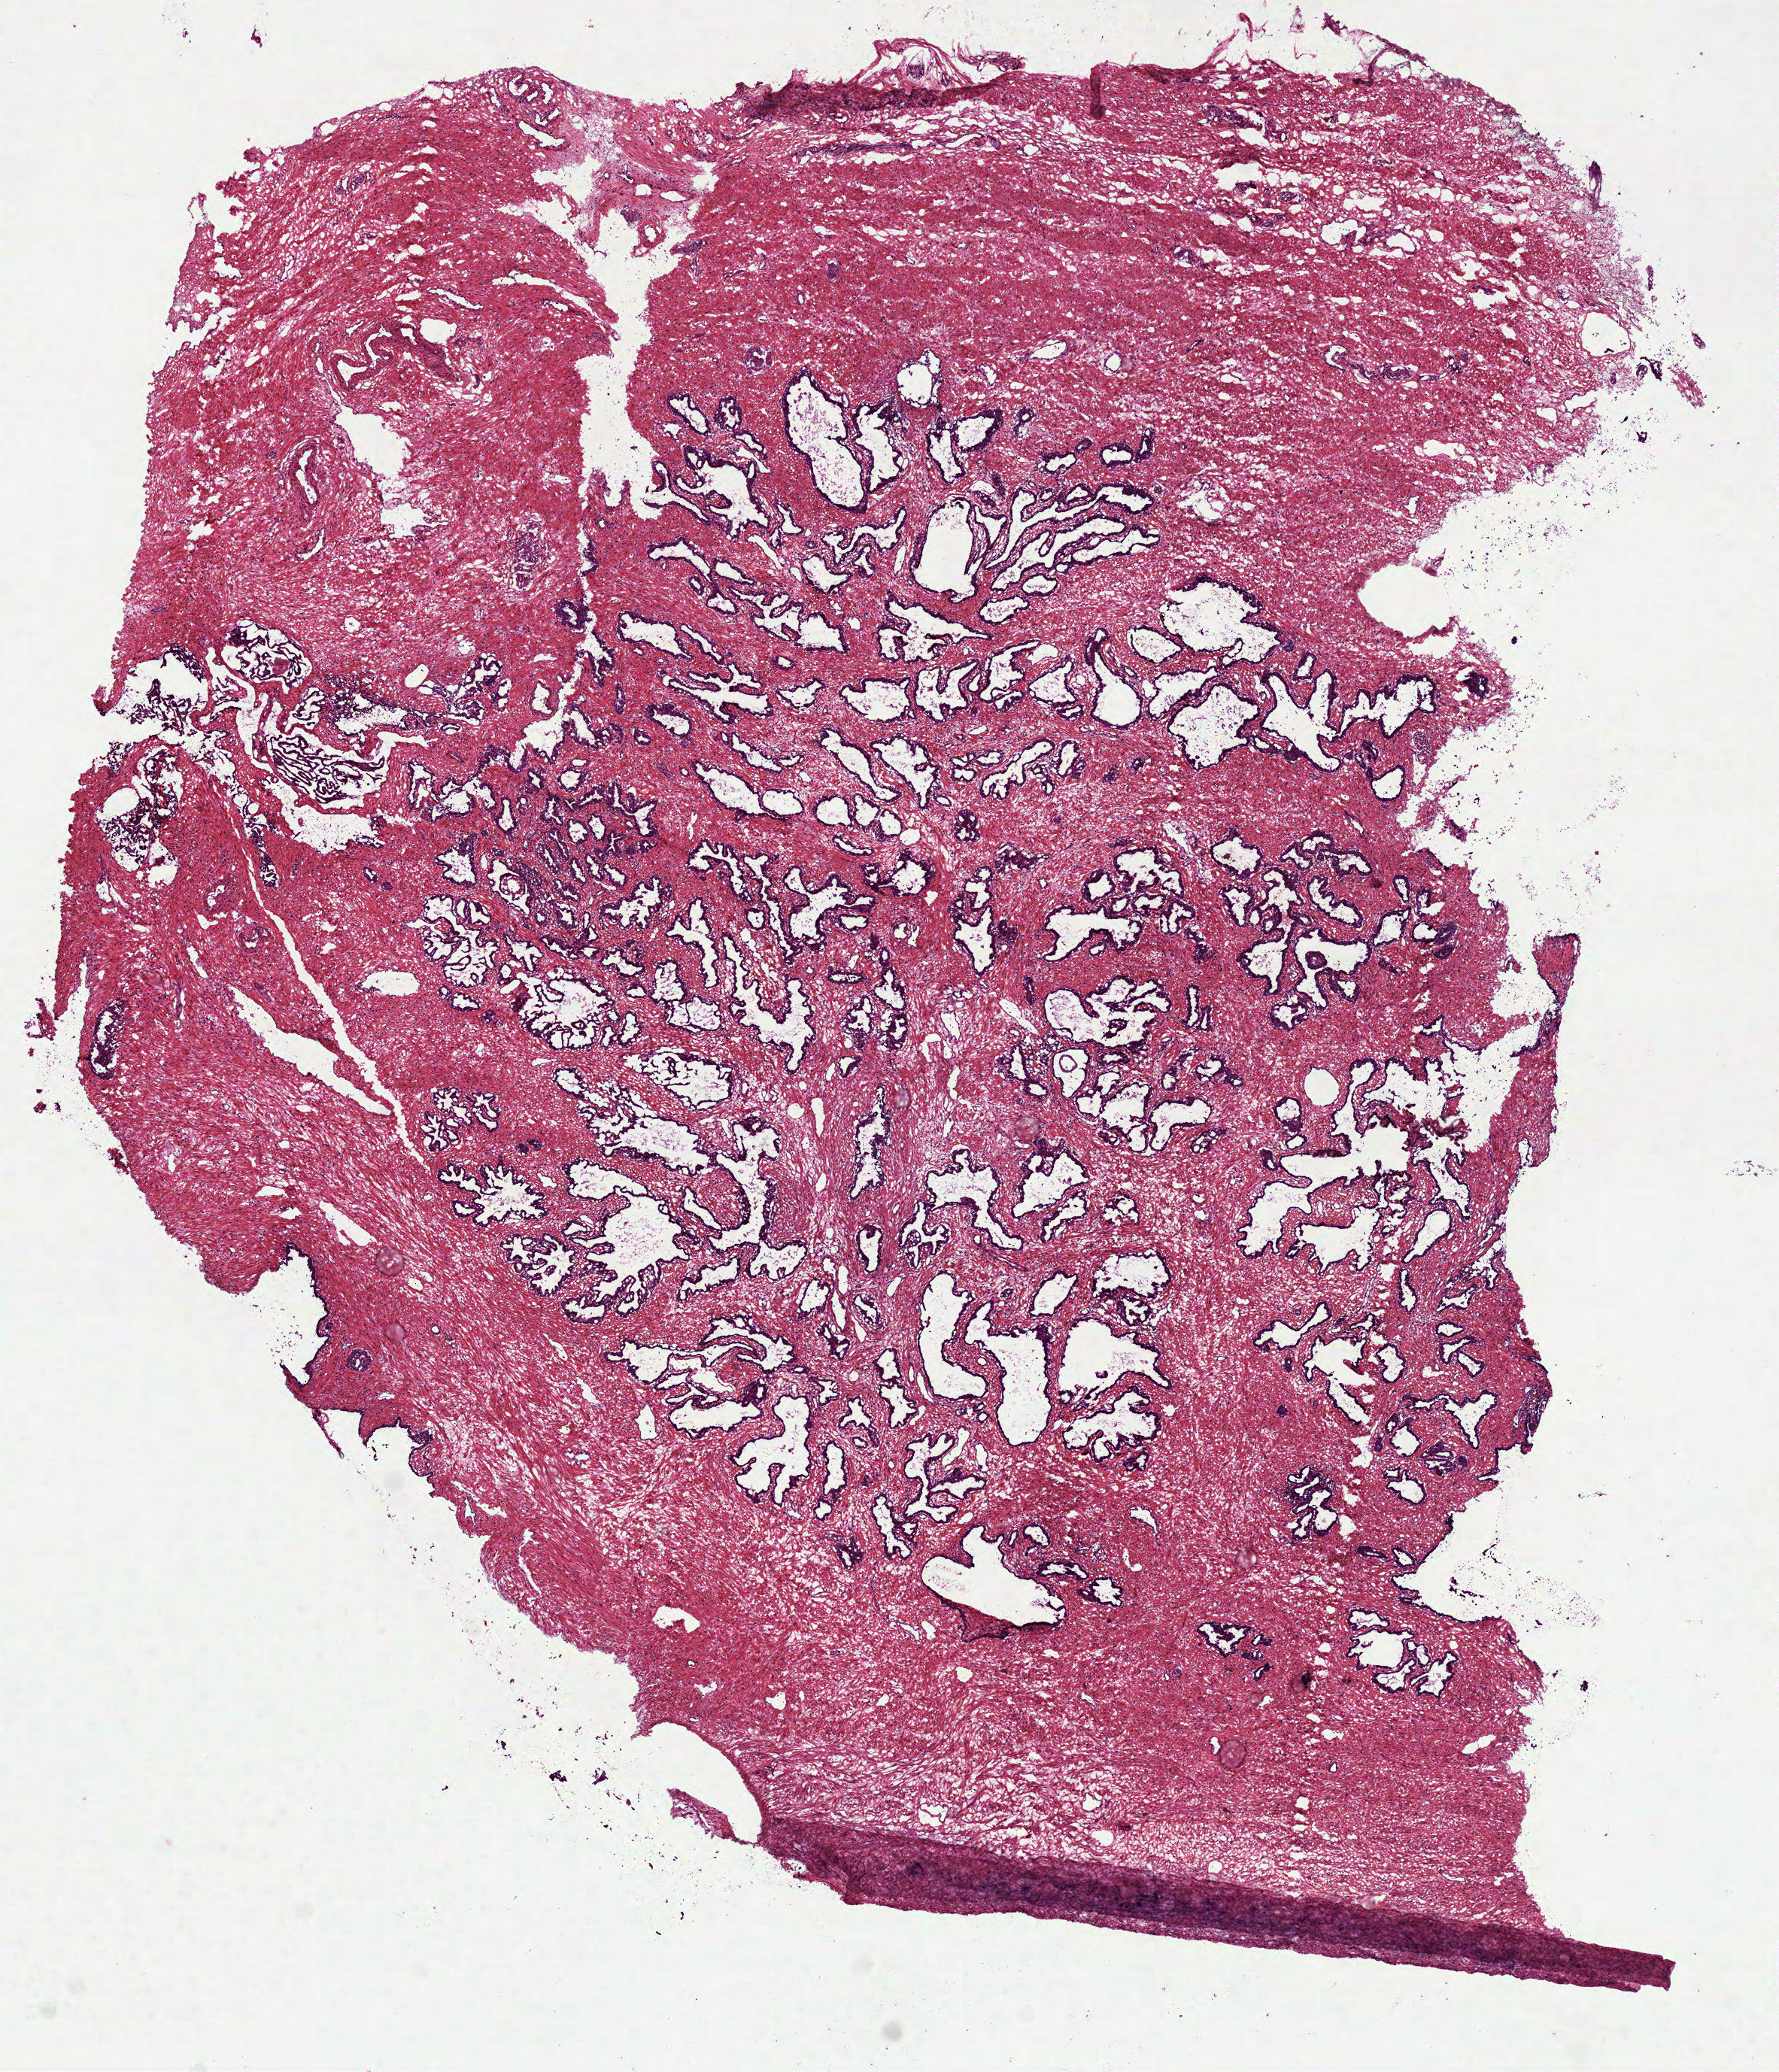
Digitized H&E-stained tissue section (whole slide), shown as a low-resolution overview of the whole scanned area (about 9.5 x 11.1 mm, from a 40x scan). Frozen section from the top of the tissue portion. Sample: solid tissue normal (non-tumour tissue), prostate. Male patient; age at initial diagnosis 66 years.
This section: solid tissue normal (non-tumour) sample from the same patient. Patient diagnosis: Acinar cell carcinoma (prostate gland).